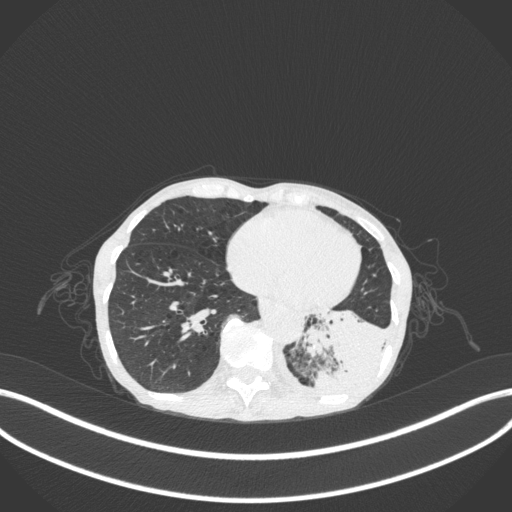
Chest CT, one axial slice; lung window (W 1500 / L -600 HU); 1 mm slice thickness; 512 × 512 image matrix, field of view 400 × 400 mm. Female patient, age 70 years. From the clinical record (not read from this slice): clinical TNM (as recorded): T3 N0 M0; histopathological grade: G3.
Outlined on this slice (bounding box drawn by a radiologist):
- lung tumour (recorded histology: small cell carcinoma): bounding box <297,300,388,408> (left, top, right, bottom; pixels)